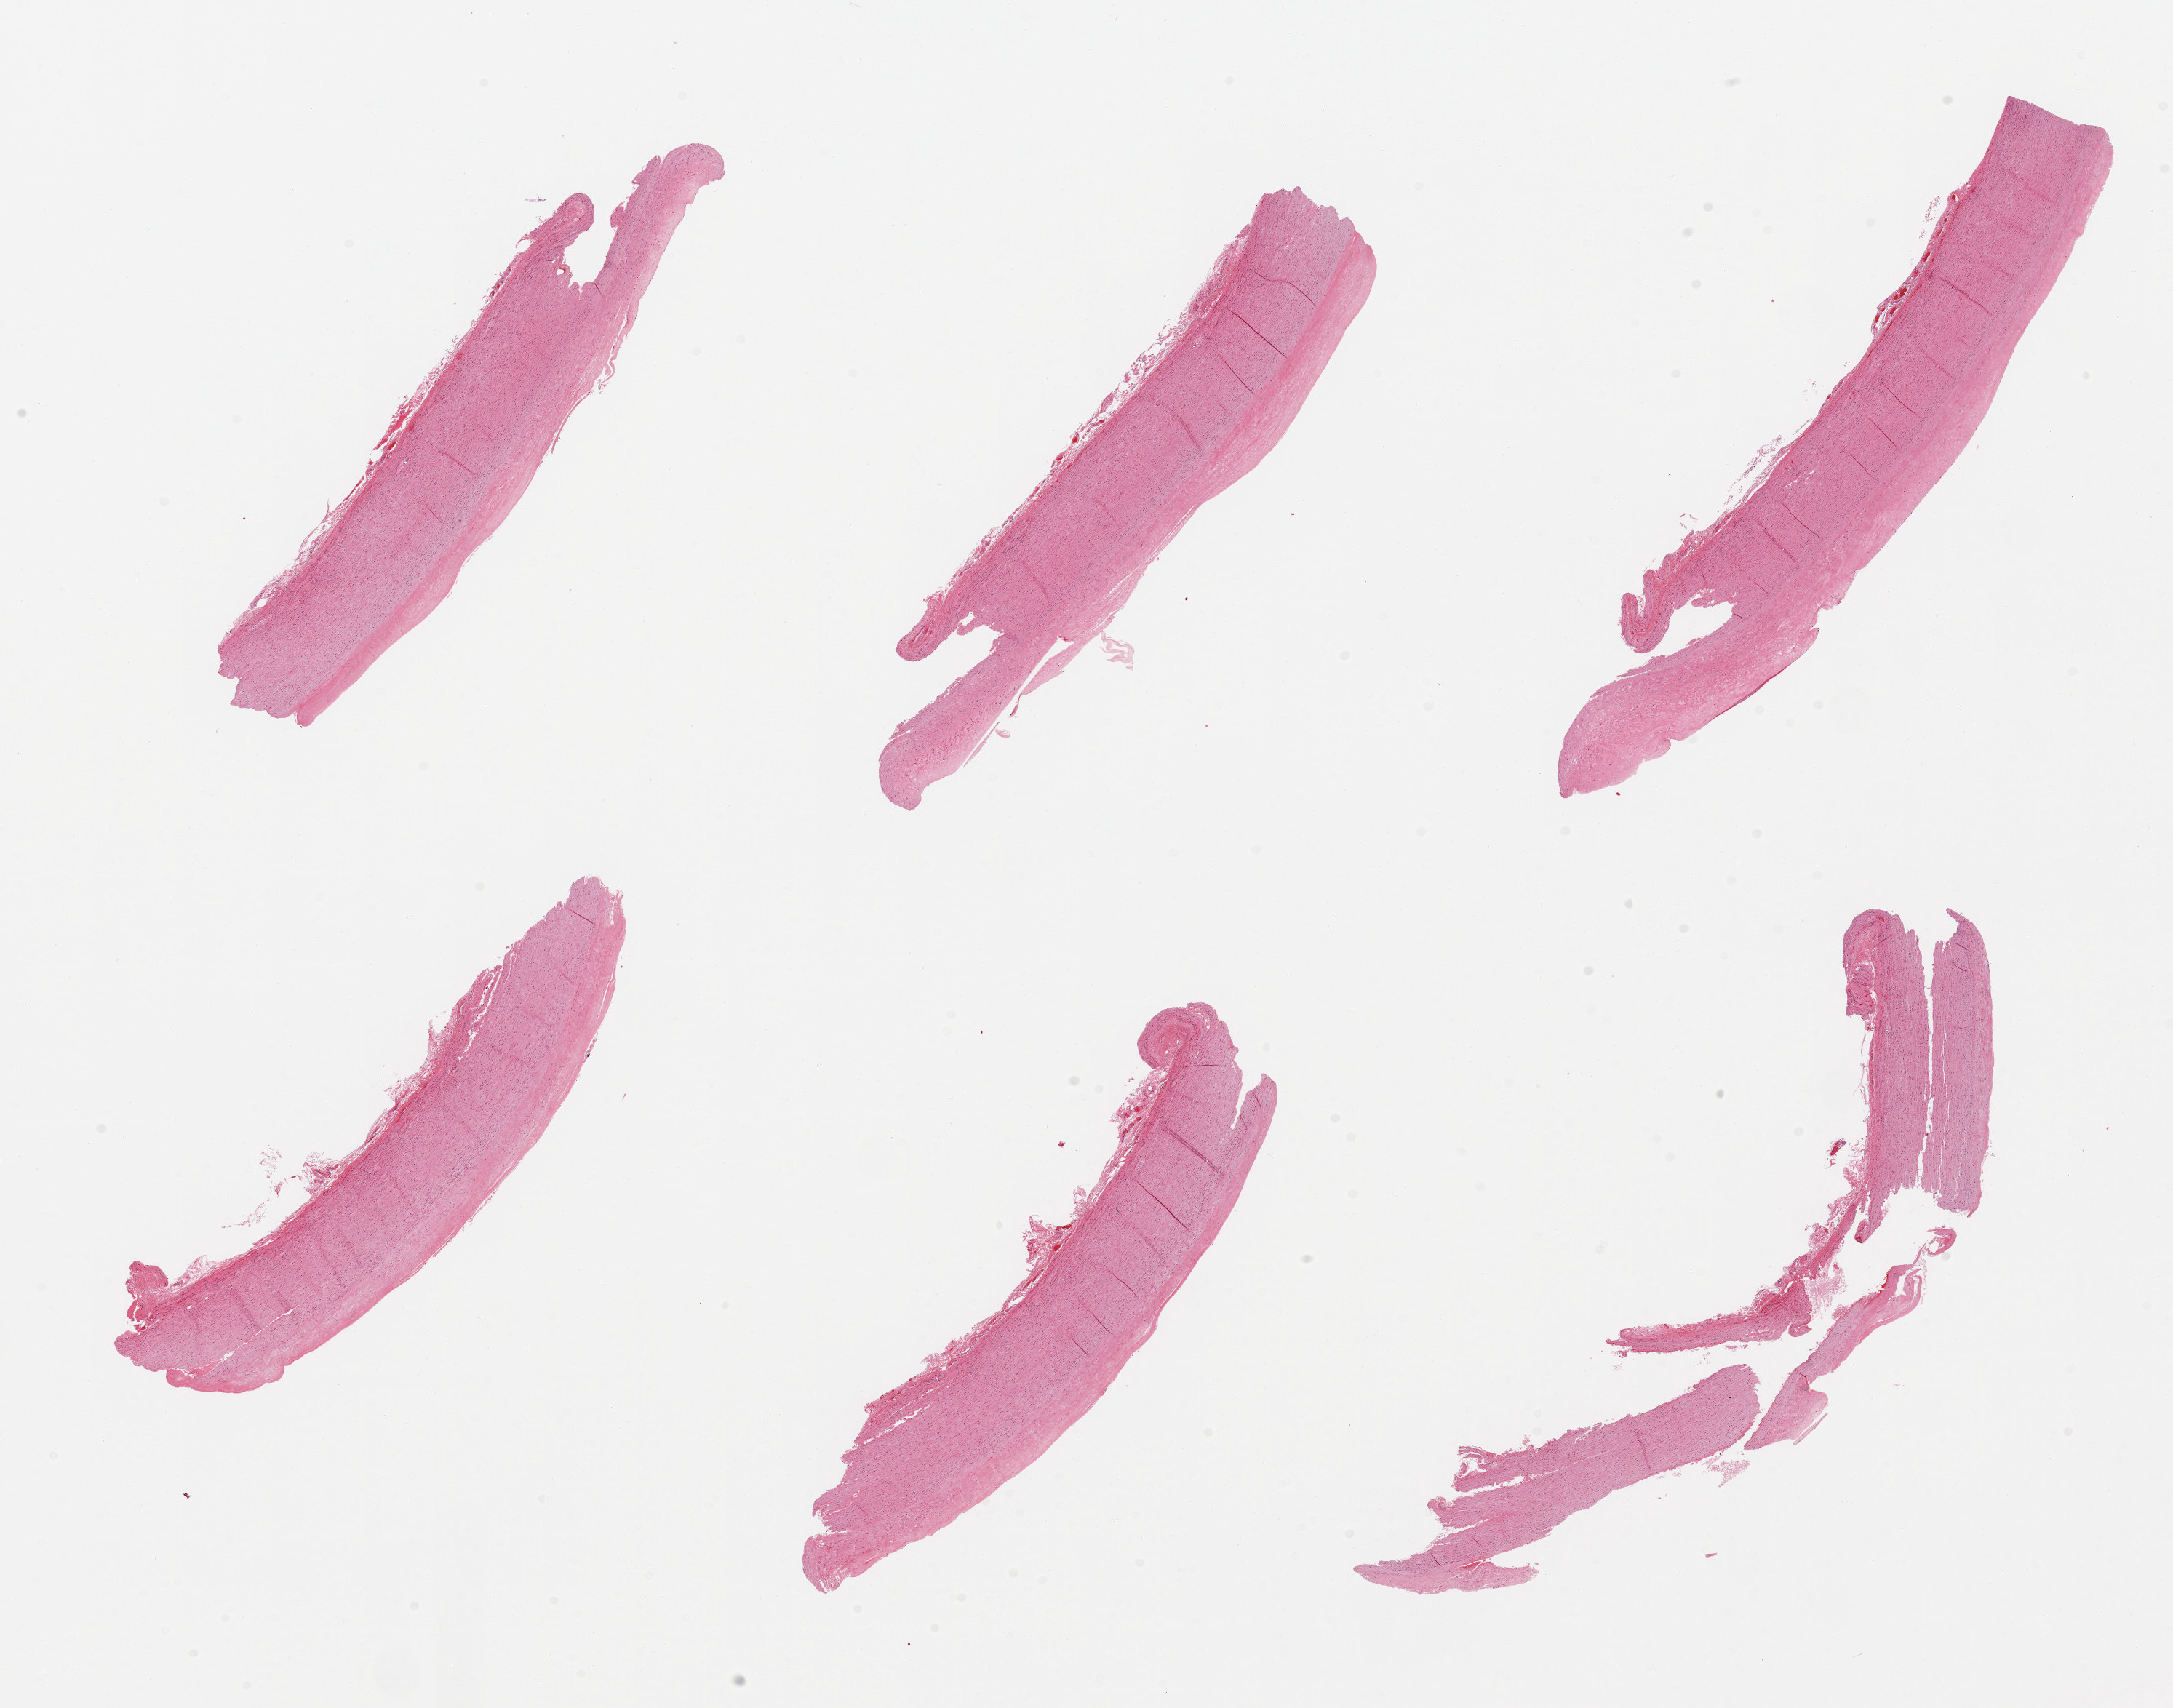
H&E whole-slide image, brightfield — low-resolution overview of the scanned area, about 23.6 x 18.6 mm. PAXgene-fixed, paraffin-embedded tissue. Sampled site (target tissue): aorta. Donor tissue sample. Donor: male.
• reviewer comment on this tissue sample: 6 pieces, atherosis up to ~0.3mm